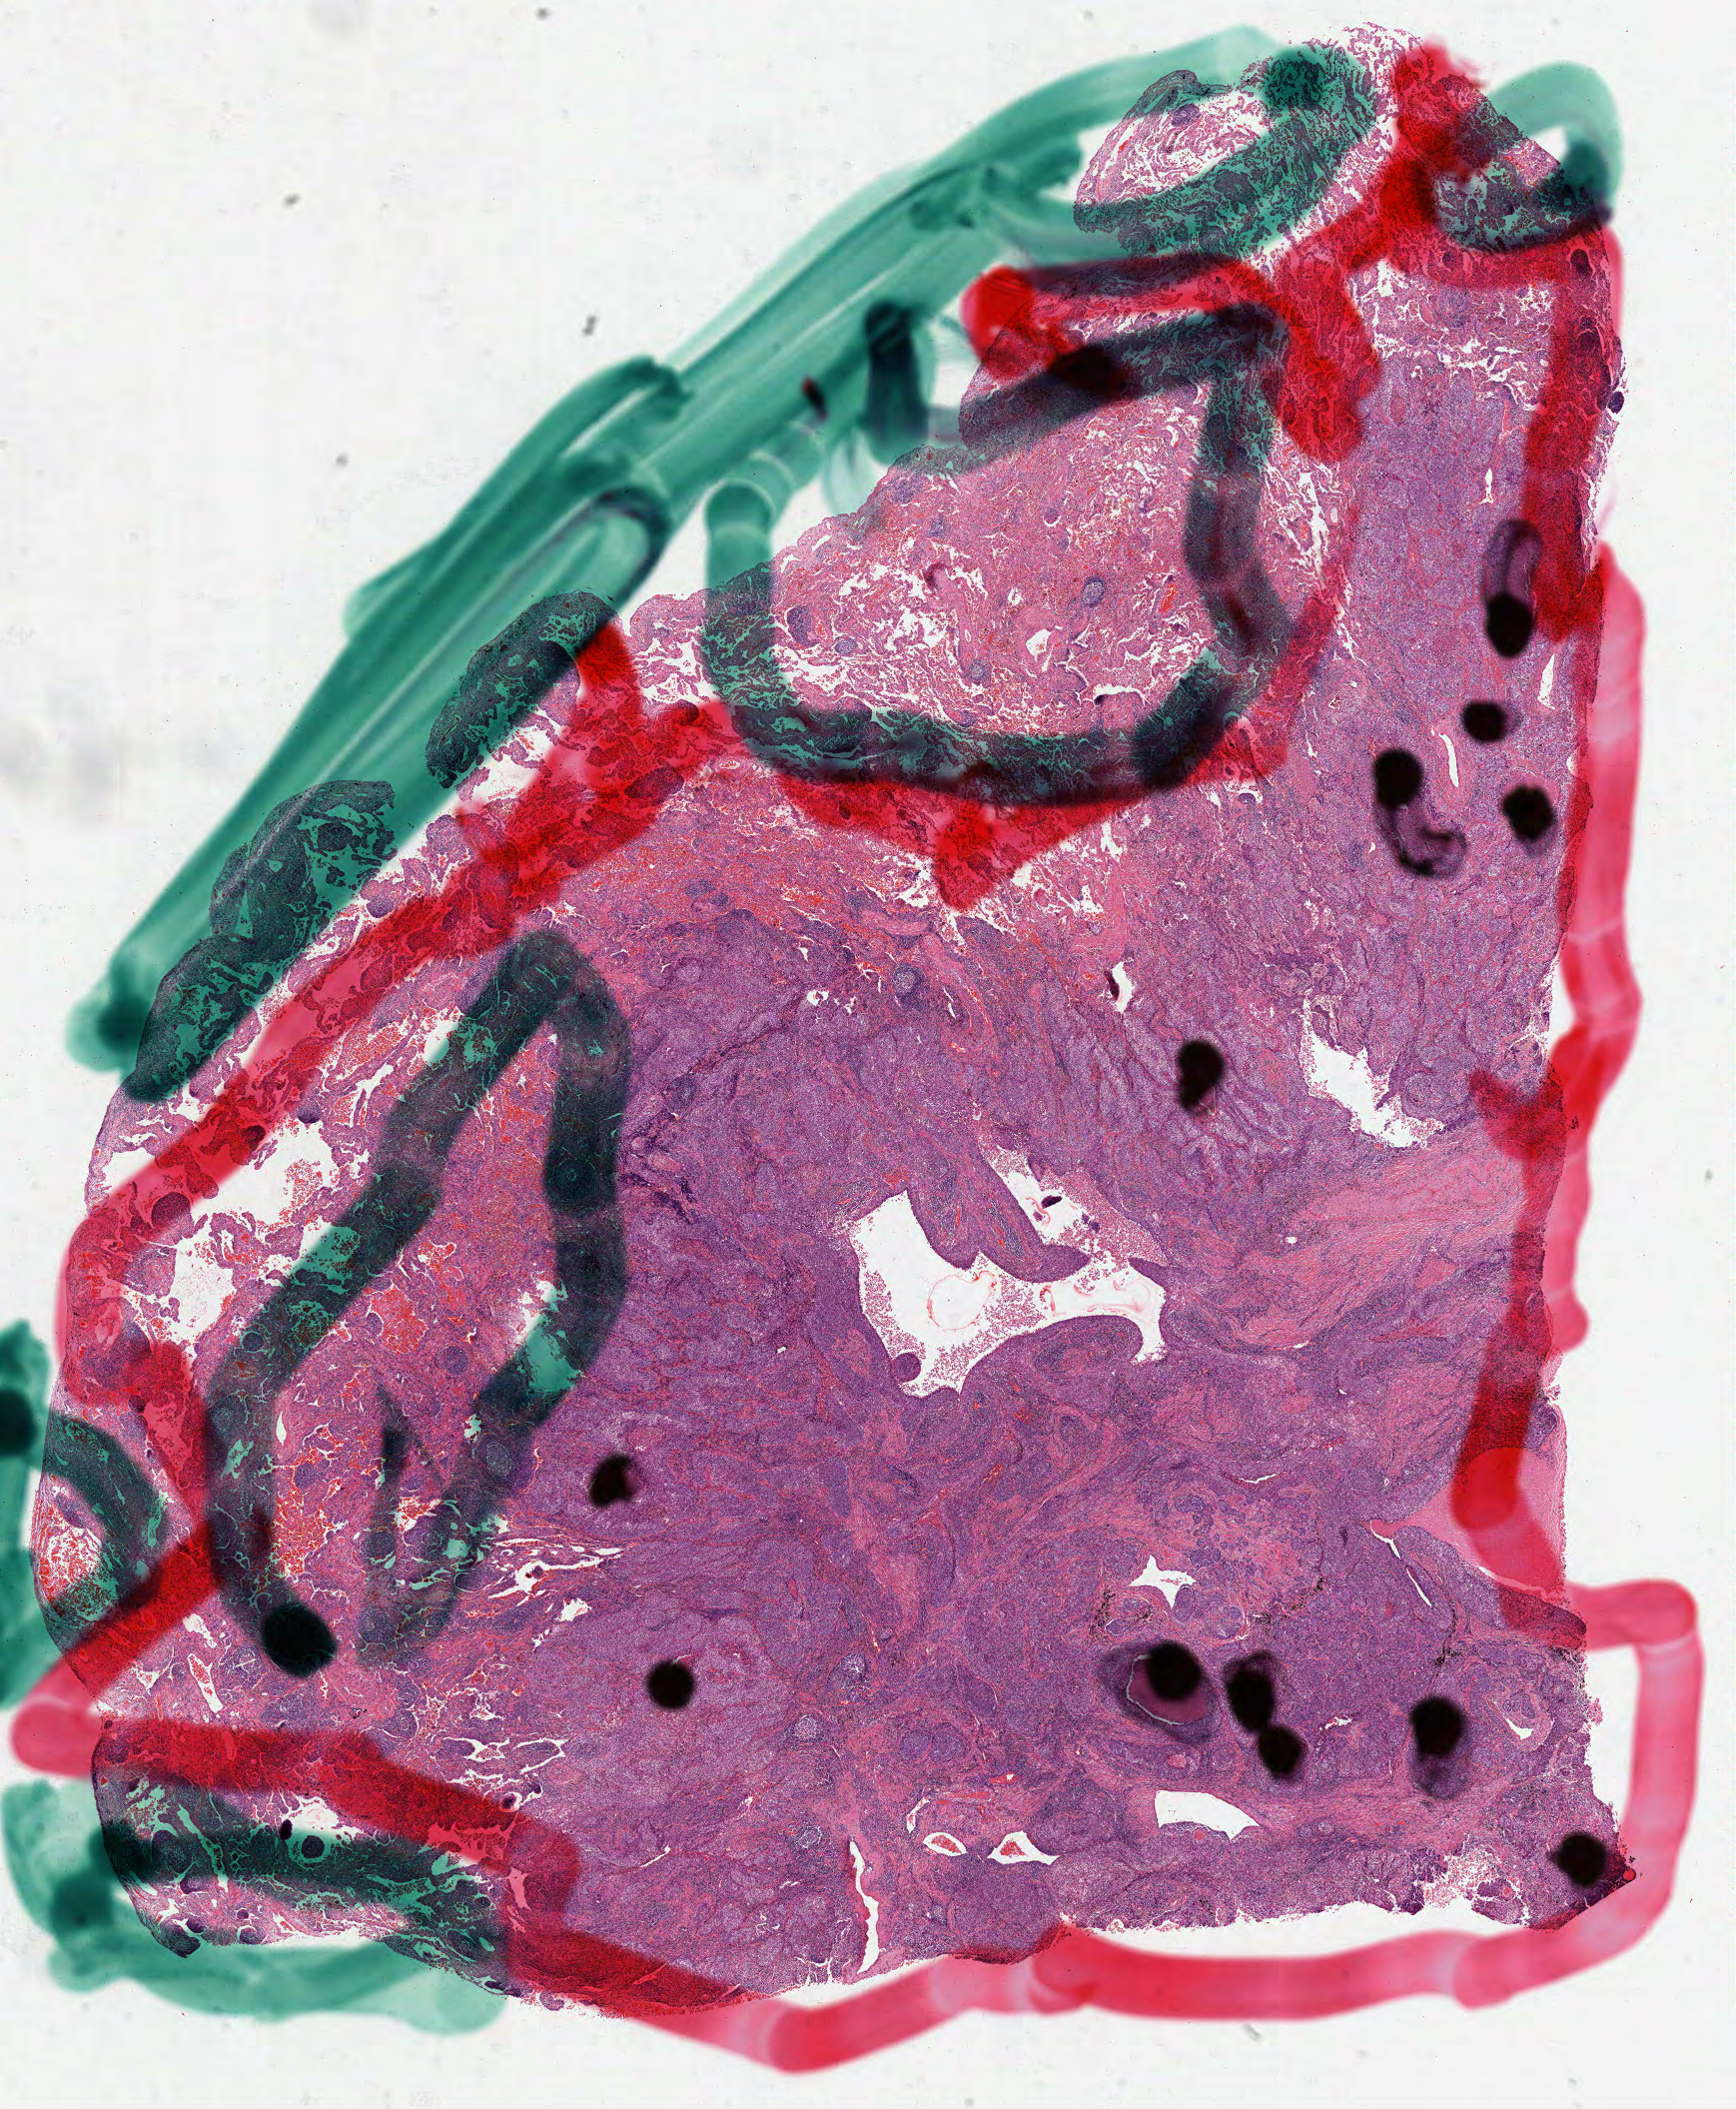
Hematoxylin and eosin (H&E) stained whole-slide image, a low-resolution overview of the entire scanned area, about 14.0 x 17.0 mm, formalin-fixed paraffin-embedded (FFPE) diagnostic section, sample: primary tumour, lung. Patient: male, age at initial diagnosis 72 years.
AJCC pathologic stage: IA. TNM: T1b N0 M0. Histologic diagnosis: Squamous cell carcinoma, NOS (upper lobe, lung).